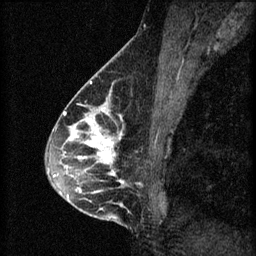
Breast MRI (dynamic contrast-enhanced), one sagittal slice; position 31 of 60 along the scan axis; 3 images stored at this slice position (order not interpretable as contrast timing); 1.5 T; TE 4.2 ms, TR 8.2 ms; 2 mm slice thickness; 256 × 256 image matrix, field of view 180 × 180 mm. Patient: female, 45 years.
Outlined on this slice (semi-automatically segmented with operator editing):
- analysis volume of interest (the breast-tissue region the enhancement analysis was run in; not a lesion): bounding box [x1, y1, x2, y2] px = [54, 104, 159, 217]
- tumour enhancement mask (voxels above the 70 % enhancement threshold inside the analysis volume of interest): [54, 104, 125, 207]